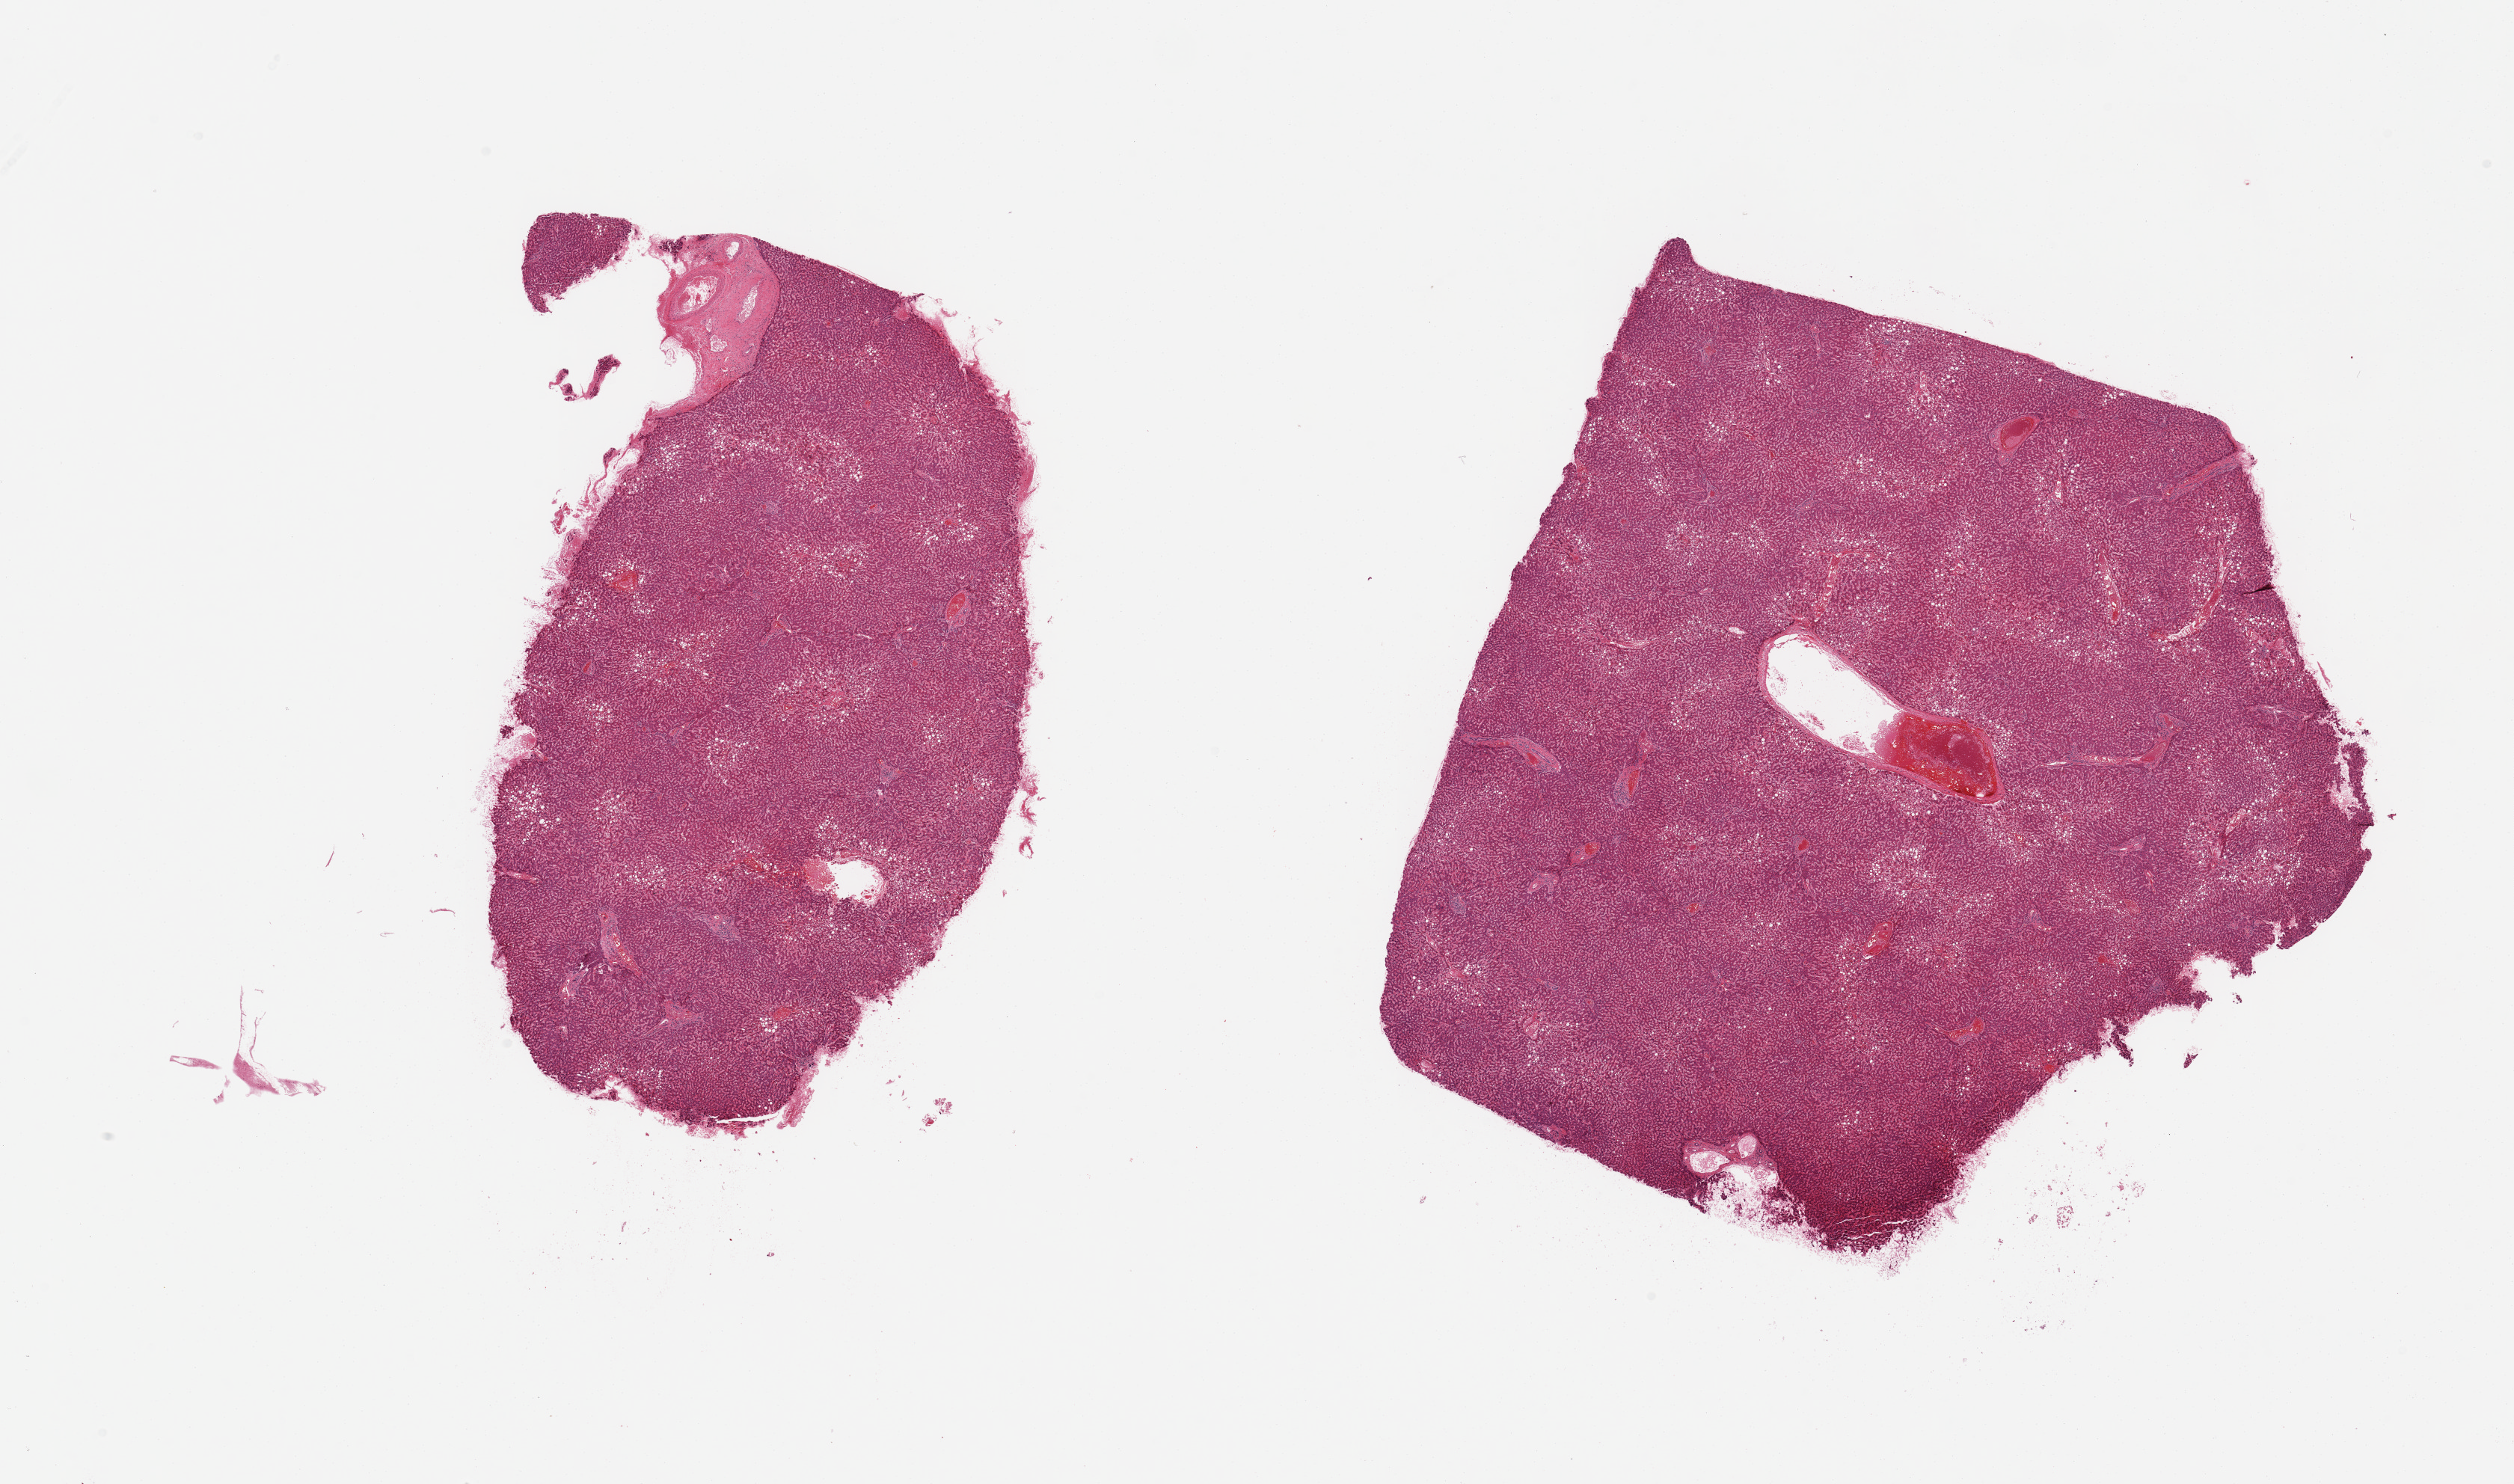
Whole-slide image, hematoxylin and eosin (H&E) stain — shown as a low-resolution overview of the whole scanned area (about 26.6 x 15.7 mm, from a 20x scan); PAXgene-fixed paraffin-embedded (PFPE) section; target tissue: liver; tissue donor sample. Donor sex: male.
• review note (as recorded): 2 pieces; mild to moderate steatosis